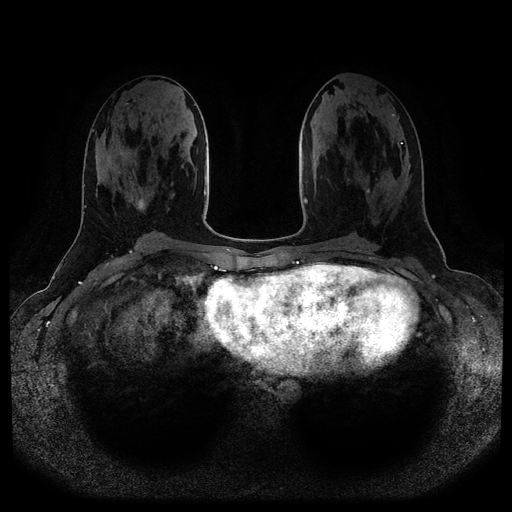
Breast MRI (dynamic contrast-enhanced, multi-phase), one axial slice; slice 45 of 116 in the series (ordered by position); dynamic contrast-enhanced series, time point 2 of 5 at this slice position (early post-contrast); 1.5 T; TE 2.6 ms, TR 5.2 ms; 2 mm slice thickness; 512 × 512 image matrix, field of view 380 × 380 mm. Patient: female, 25 years.
Outlined on this slice (semi-automatic segmentation, software-assisted and operator-edited):
- breast lesion (labelled benign in the annotation): bounding box (x1, y1, x2, y2) in pixels: (139, 199, 145, 209)